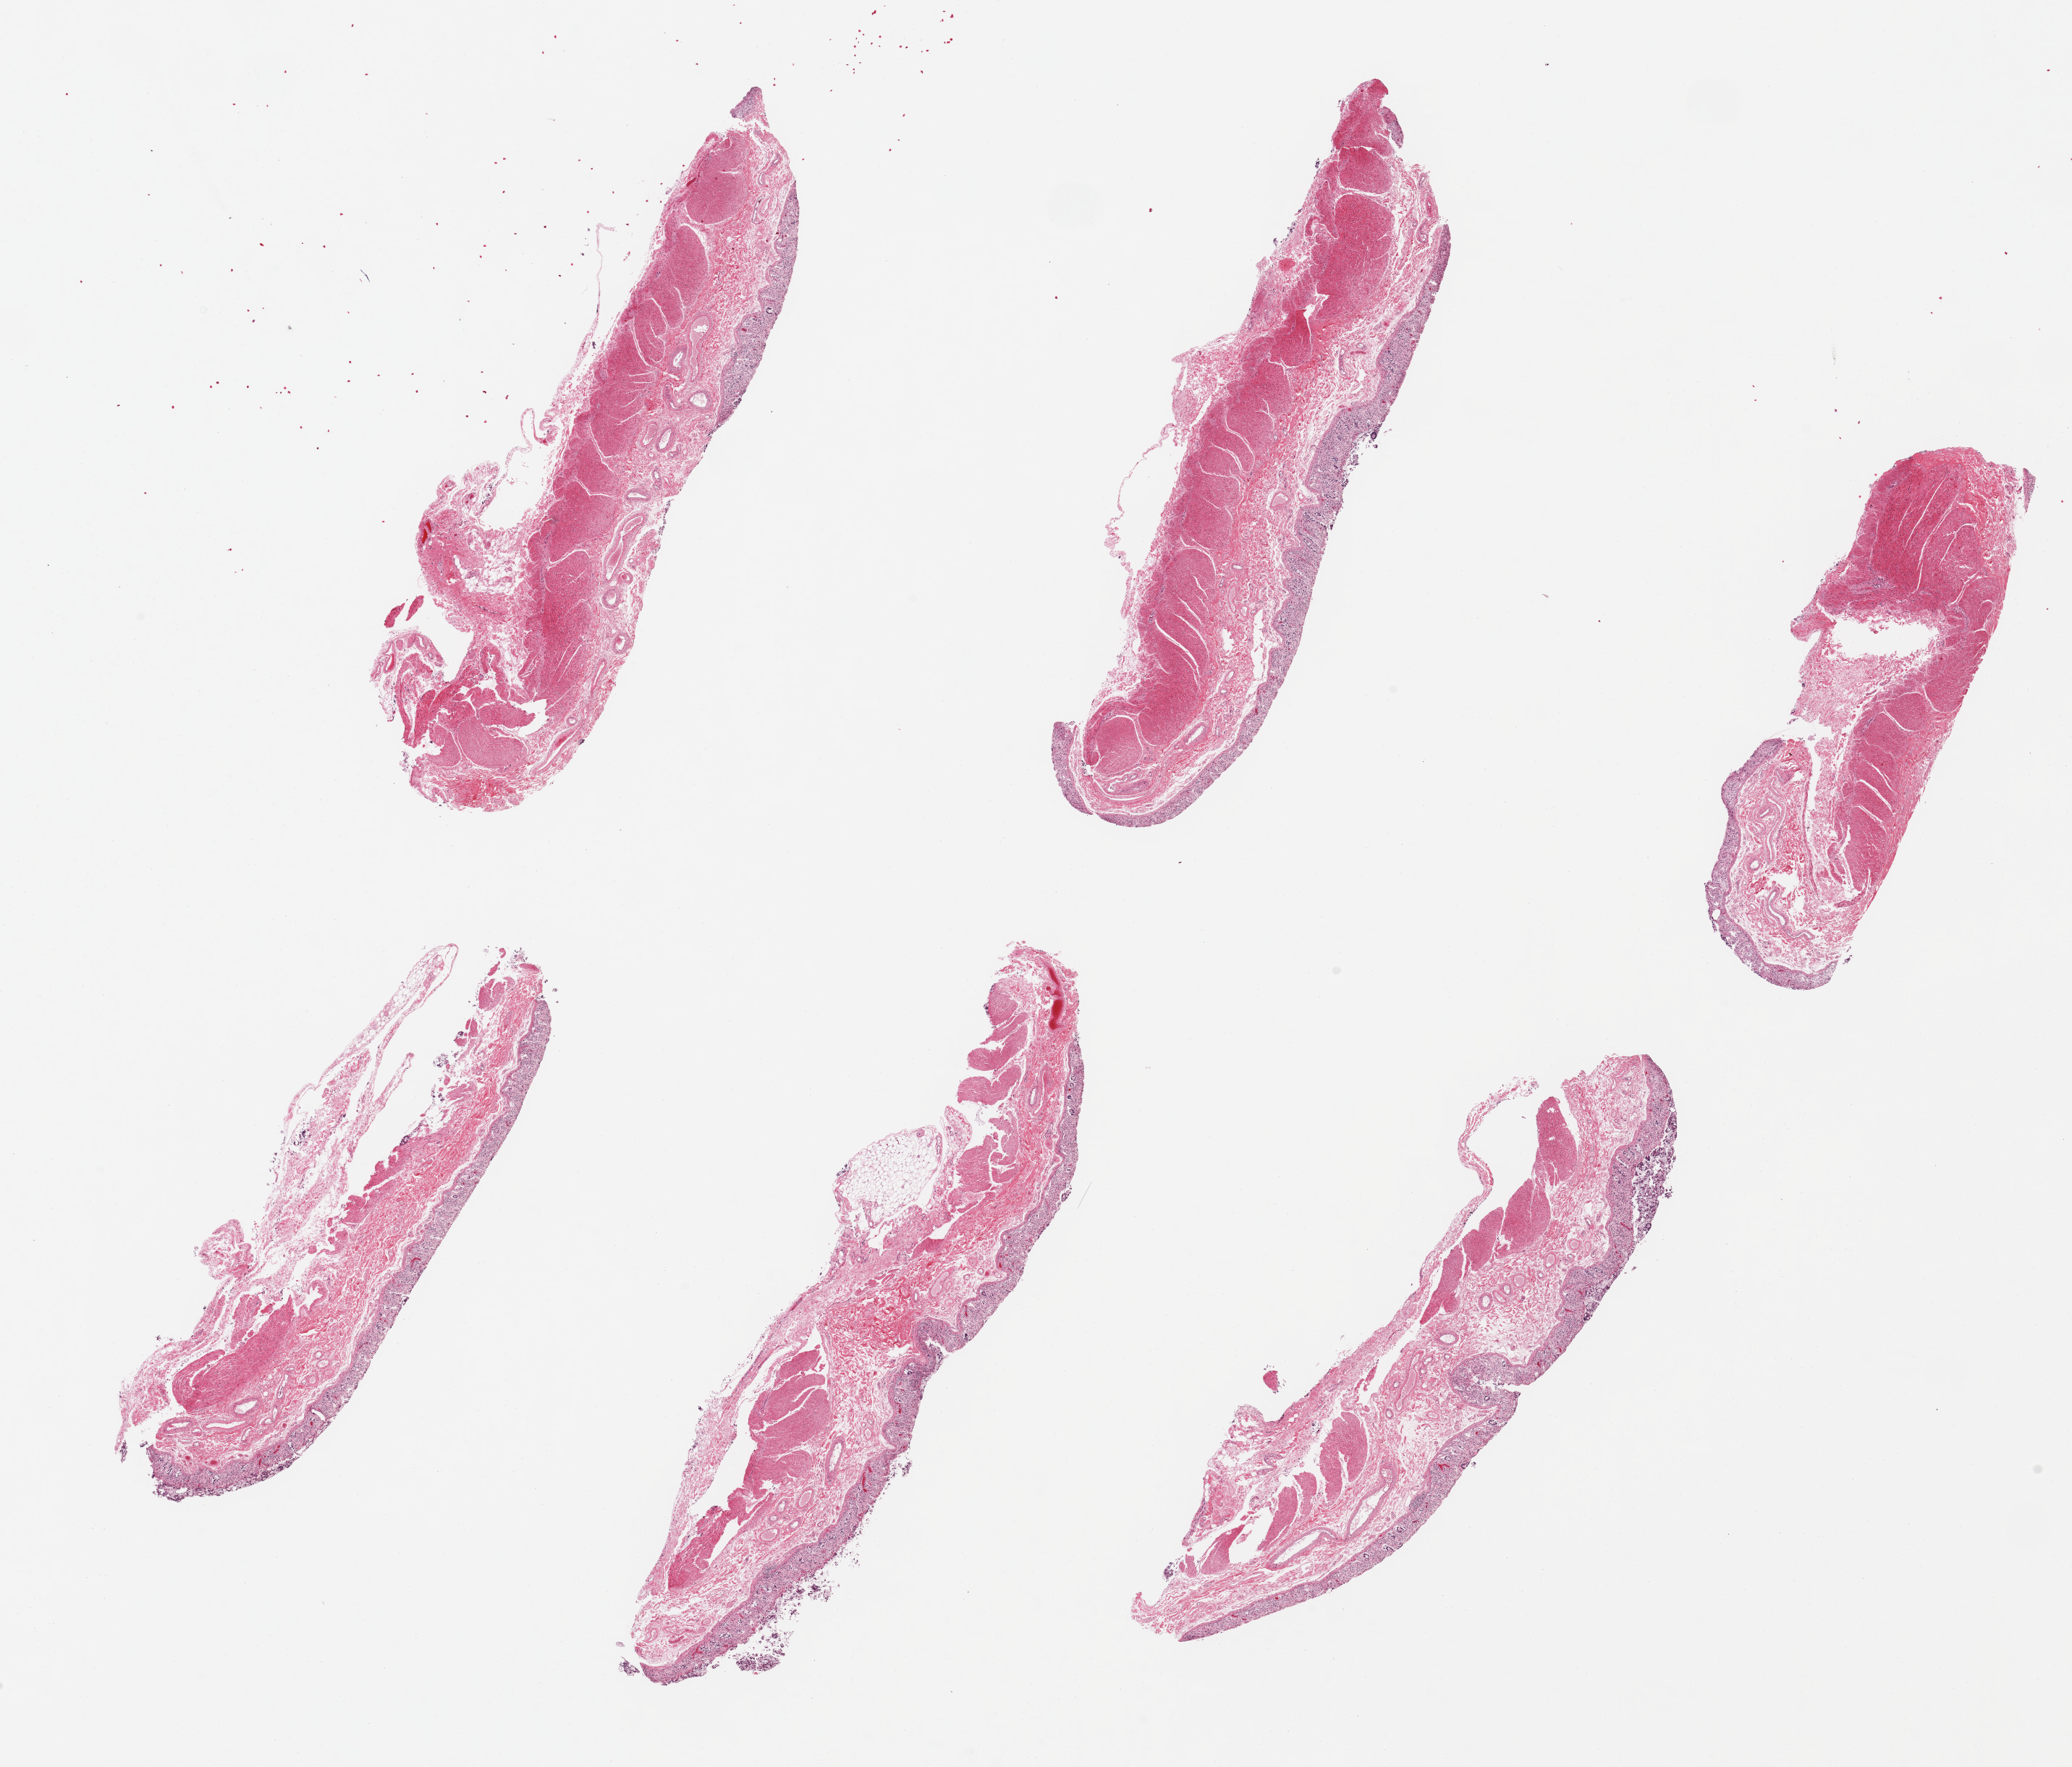
Whole-slide image, hematoxylin and eosin (H&E) stain, a low-resolution overview of the entire scanned area, about 22.6 x 19.3 mm, PAXgene-fixed, paraffin-embedded tissue, target tissue: transverse colon, tissue donor sample. Donor sex: female.
• reviewer comment on this tissue sample: 6 pieces up to 8x2 mm; mucosa totally autolyzed; wall moderately autolyzed